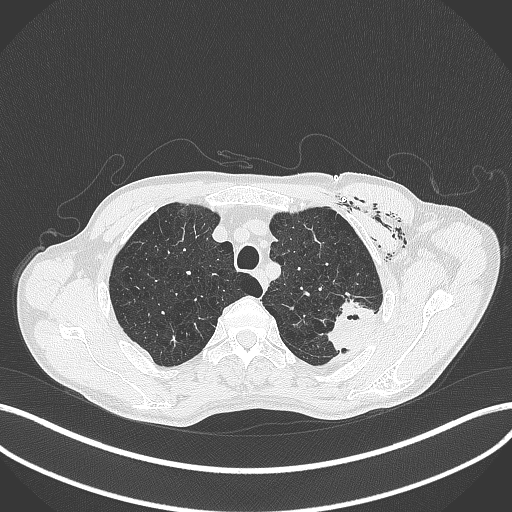
Chest CT, one axial slice. Slice 340 of 457 in the series (ordered by position). Reconstruction kernel B70f. Lung window (W 1500 / L -600 HU). 1 mm slice thickness. 512 × 512 image matrix, field of view 400 × 400 mm. Patient: male, 58 years. From the clinical record (not read from this slice): clinical TNM (as recorded): T3 N0 M0.
Structures marked on this image (bounding box drawn by a radiologist):
- lung tumour (recorded histology: adenocarcinoma): box from (x=319, y=296) to (x=380, y=351) px